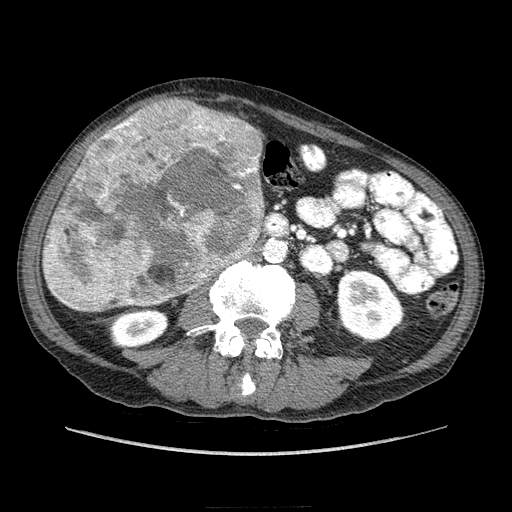
Contrast-enhanced abdominal CT (liver protocol), one axial slice; position 69 of 218 along the scan axis; reconstruction kernel STANDARD; 100 kVp; soft-tissue window (W 400 / L 40 HU); 512 × 512 image matrix. From the clinical record (not read from this slice): diagnosis: hepatocellular carcinoma (patient treated with transarterial chemoembolisation; whether this scan precedes or follows treatment is not stated here); TNM stage (as recorded): Stage-IIIA; Child-Pugh class: A.
Annotated regions visible in this slice (semi-automatically segmented with operator editing):
- liver parenchyma outside the tumour (the mass and vessels are separate outlines, so this box may not span the whole liver): bounding box <42,100,203,296> (left, top, right, bottom; pixels)
- mass: <43,100,266,311>